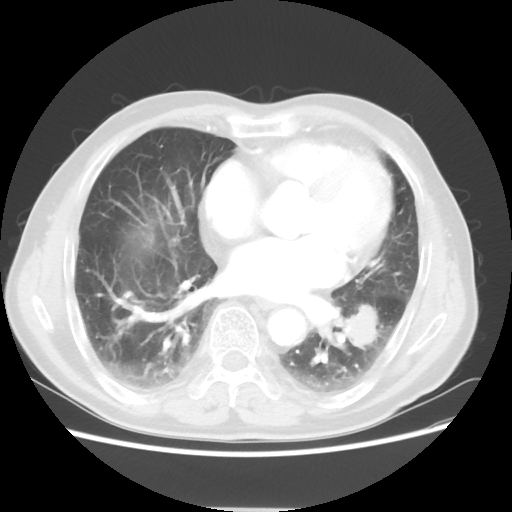
Chest CT, one axial slice; position 30 of 64 along the scan axis; reconstruction kernel STANDARD; 120 kVp; lung window (W 1500 / L -600 HU); 5 mm slice thickness; 512 × 512 image matrix. Male patient, age 71 years. From the clinical record (not read from this slice): clinical TNM (as recorded): T1c N1 M0.
Structures marked on this image (rectangle marked by the reading radiologist):
- lung tumour (recorded histology: adenocarcinoma): bounding box (x1, y1, x2, y2) in pixels: (339, 293, 378, 359)